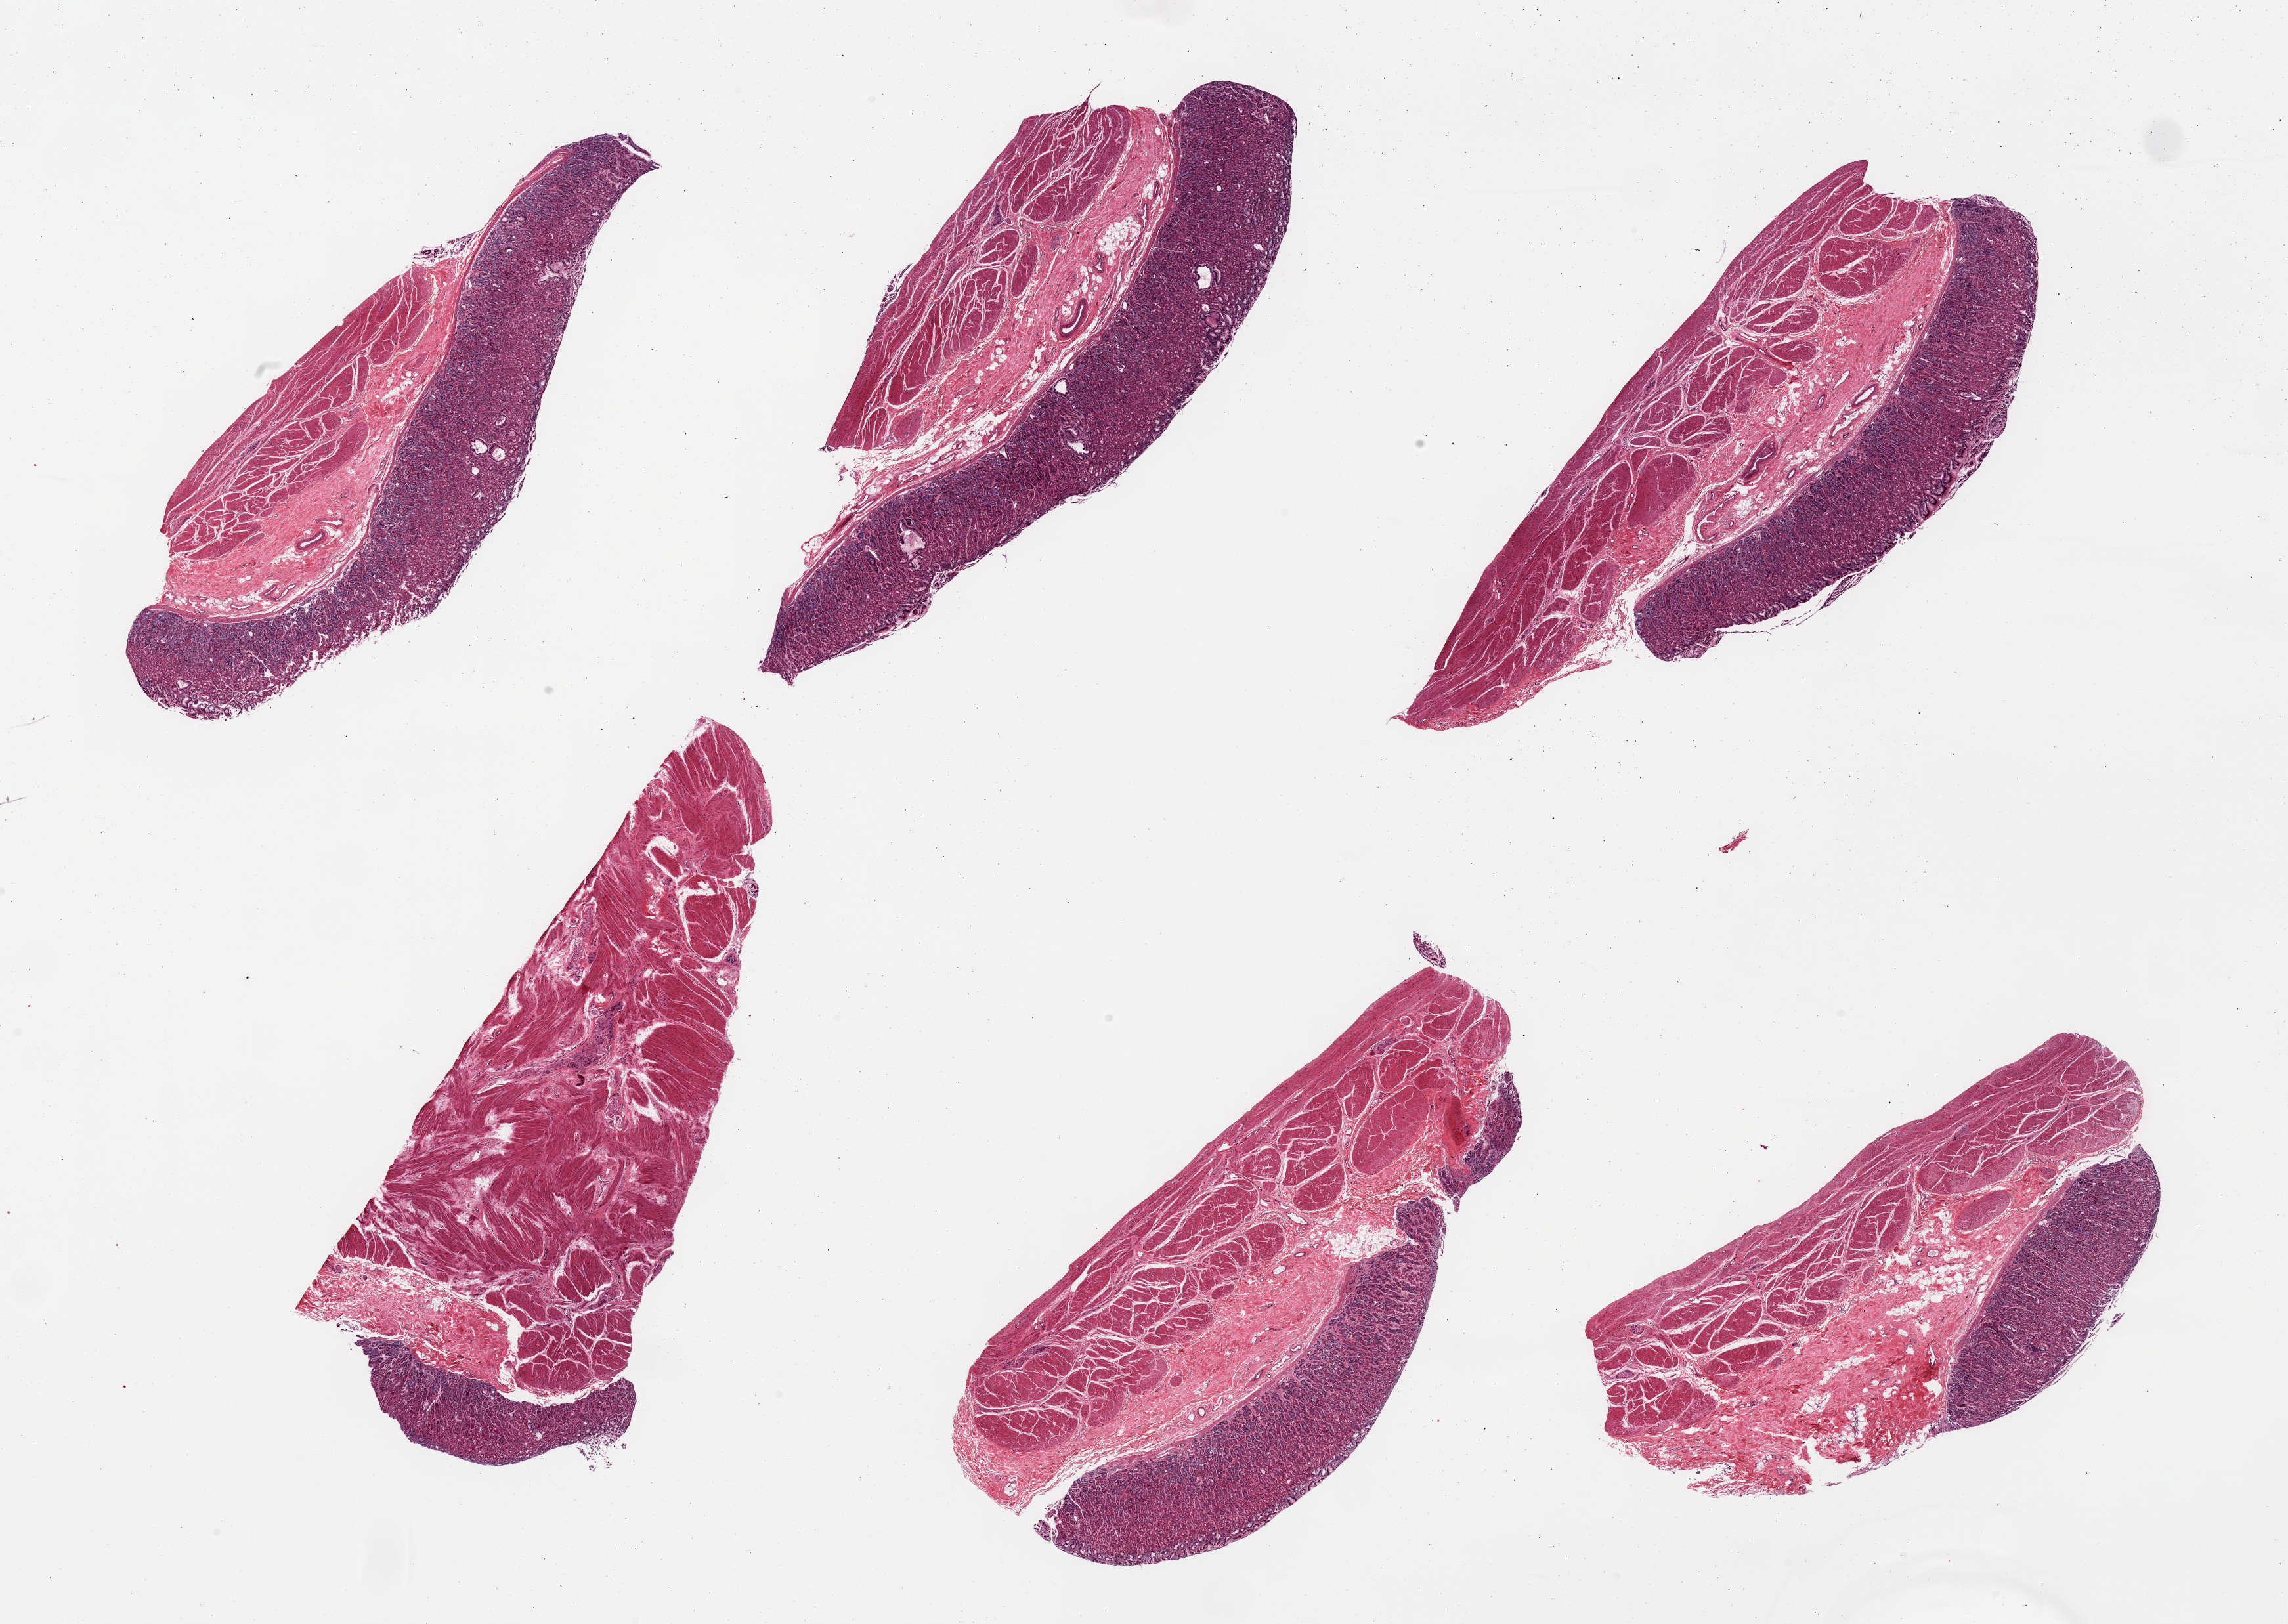
Whole-slide image, H&E stain, brightfield — shown as a low-resolution overview of the whole scanned area (about 27.6 x 19.6 mm, from a 20x scan), PAXgene-fixed, paraffin-embedded tissue, sampled site (target tissue): stomach, donor tissue sample. Donor sex: male.
Review note (as recorded): 6 pieces, mucosa well -preserved, 30-50% thickness, in some areas up to 1.3mm thick...focal deep glandular dilations, unknown etiology.